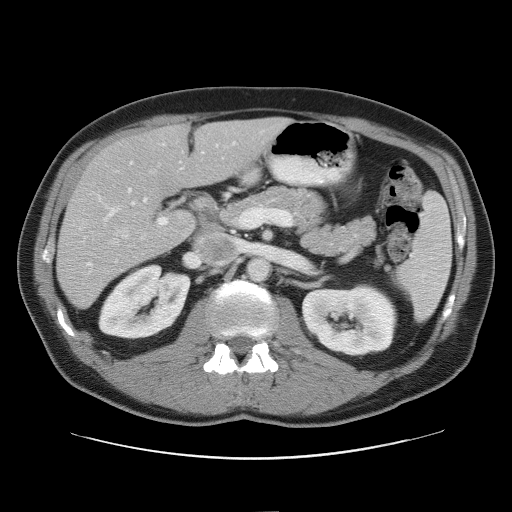
Contrast-enhanced abdominal CT, one axial slice. Position 31 of 52 along the scan axis. Reconstruction kernel STANDARD. Intravenous contrast given. Soft-tissue window (W 400 / L 40 HU). 512 × 512 image matrix. Male patient, age 70 years. From the clinical record (not read from this slice): diagnosis: colorectal cancer liver metastases, imaged before liver resection; multiple liver metastases: yes; largest metastasis: 4 cm.
Outlined on this slice (expert manual segmentation):
- hepatic veins: bounding box [x1, y1, x2, y2] px = [78, 170, 155, 267]
- liver: [58, 119, 286, 307]
- planned liver remnant (the part of the liver to remain after resection): [114, 118, 286, 188]
- portal vein (with intrahepatic branches): [109, 143, 235, 226]